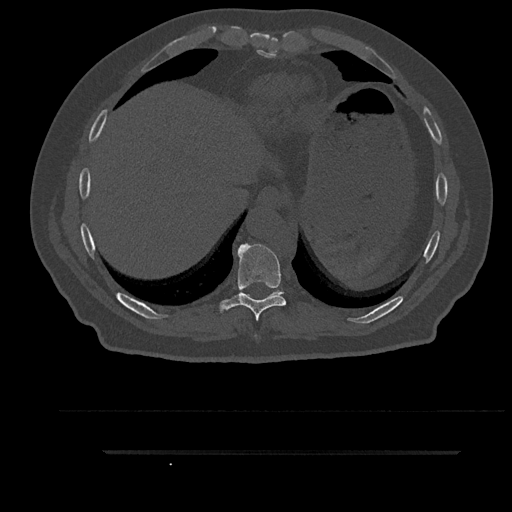
CT including the spine, one axial slice. Position 421 of 797 along the scan axis. Reconstruction kernel Br40s/3. 120 kVp. Bone window (W 1800 / L 400 HU). 512 × 512 image matrix. Patient: male, 63 years. Case-level facts recorded for this patient, not image findings: primary cancer: renal; vertebrae with lytic lesions (as recorded): T8.
Outlined on this slice (semi-automatic segmentation, software-assisted and operator-edited):
- T10 vertebra: box from (x=271, y=289) to (x=283, y=296) px
- T9 vertebra: (x=218, y=243)–(x=294, y=321)